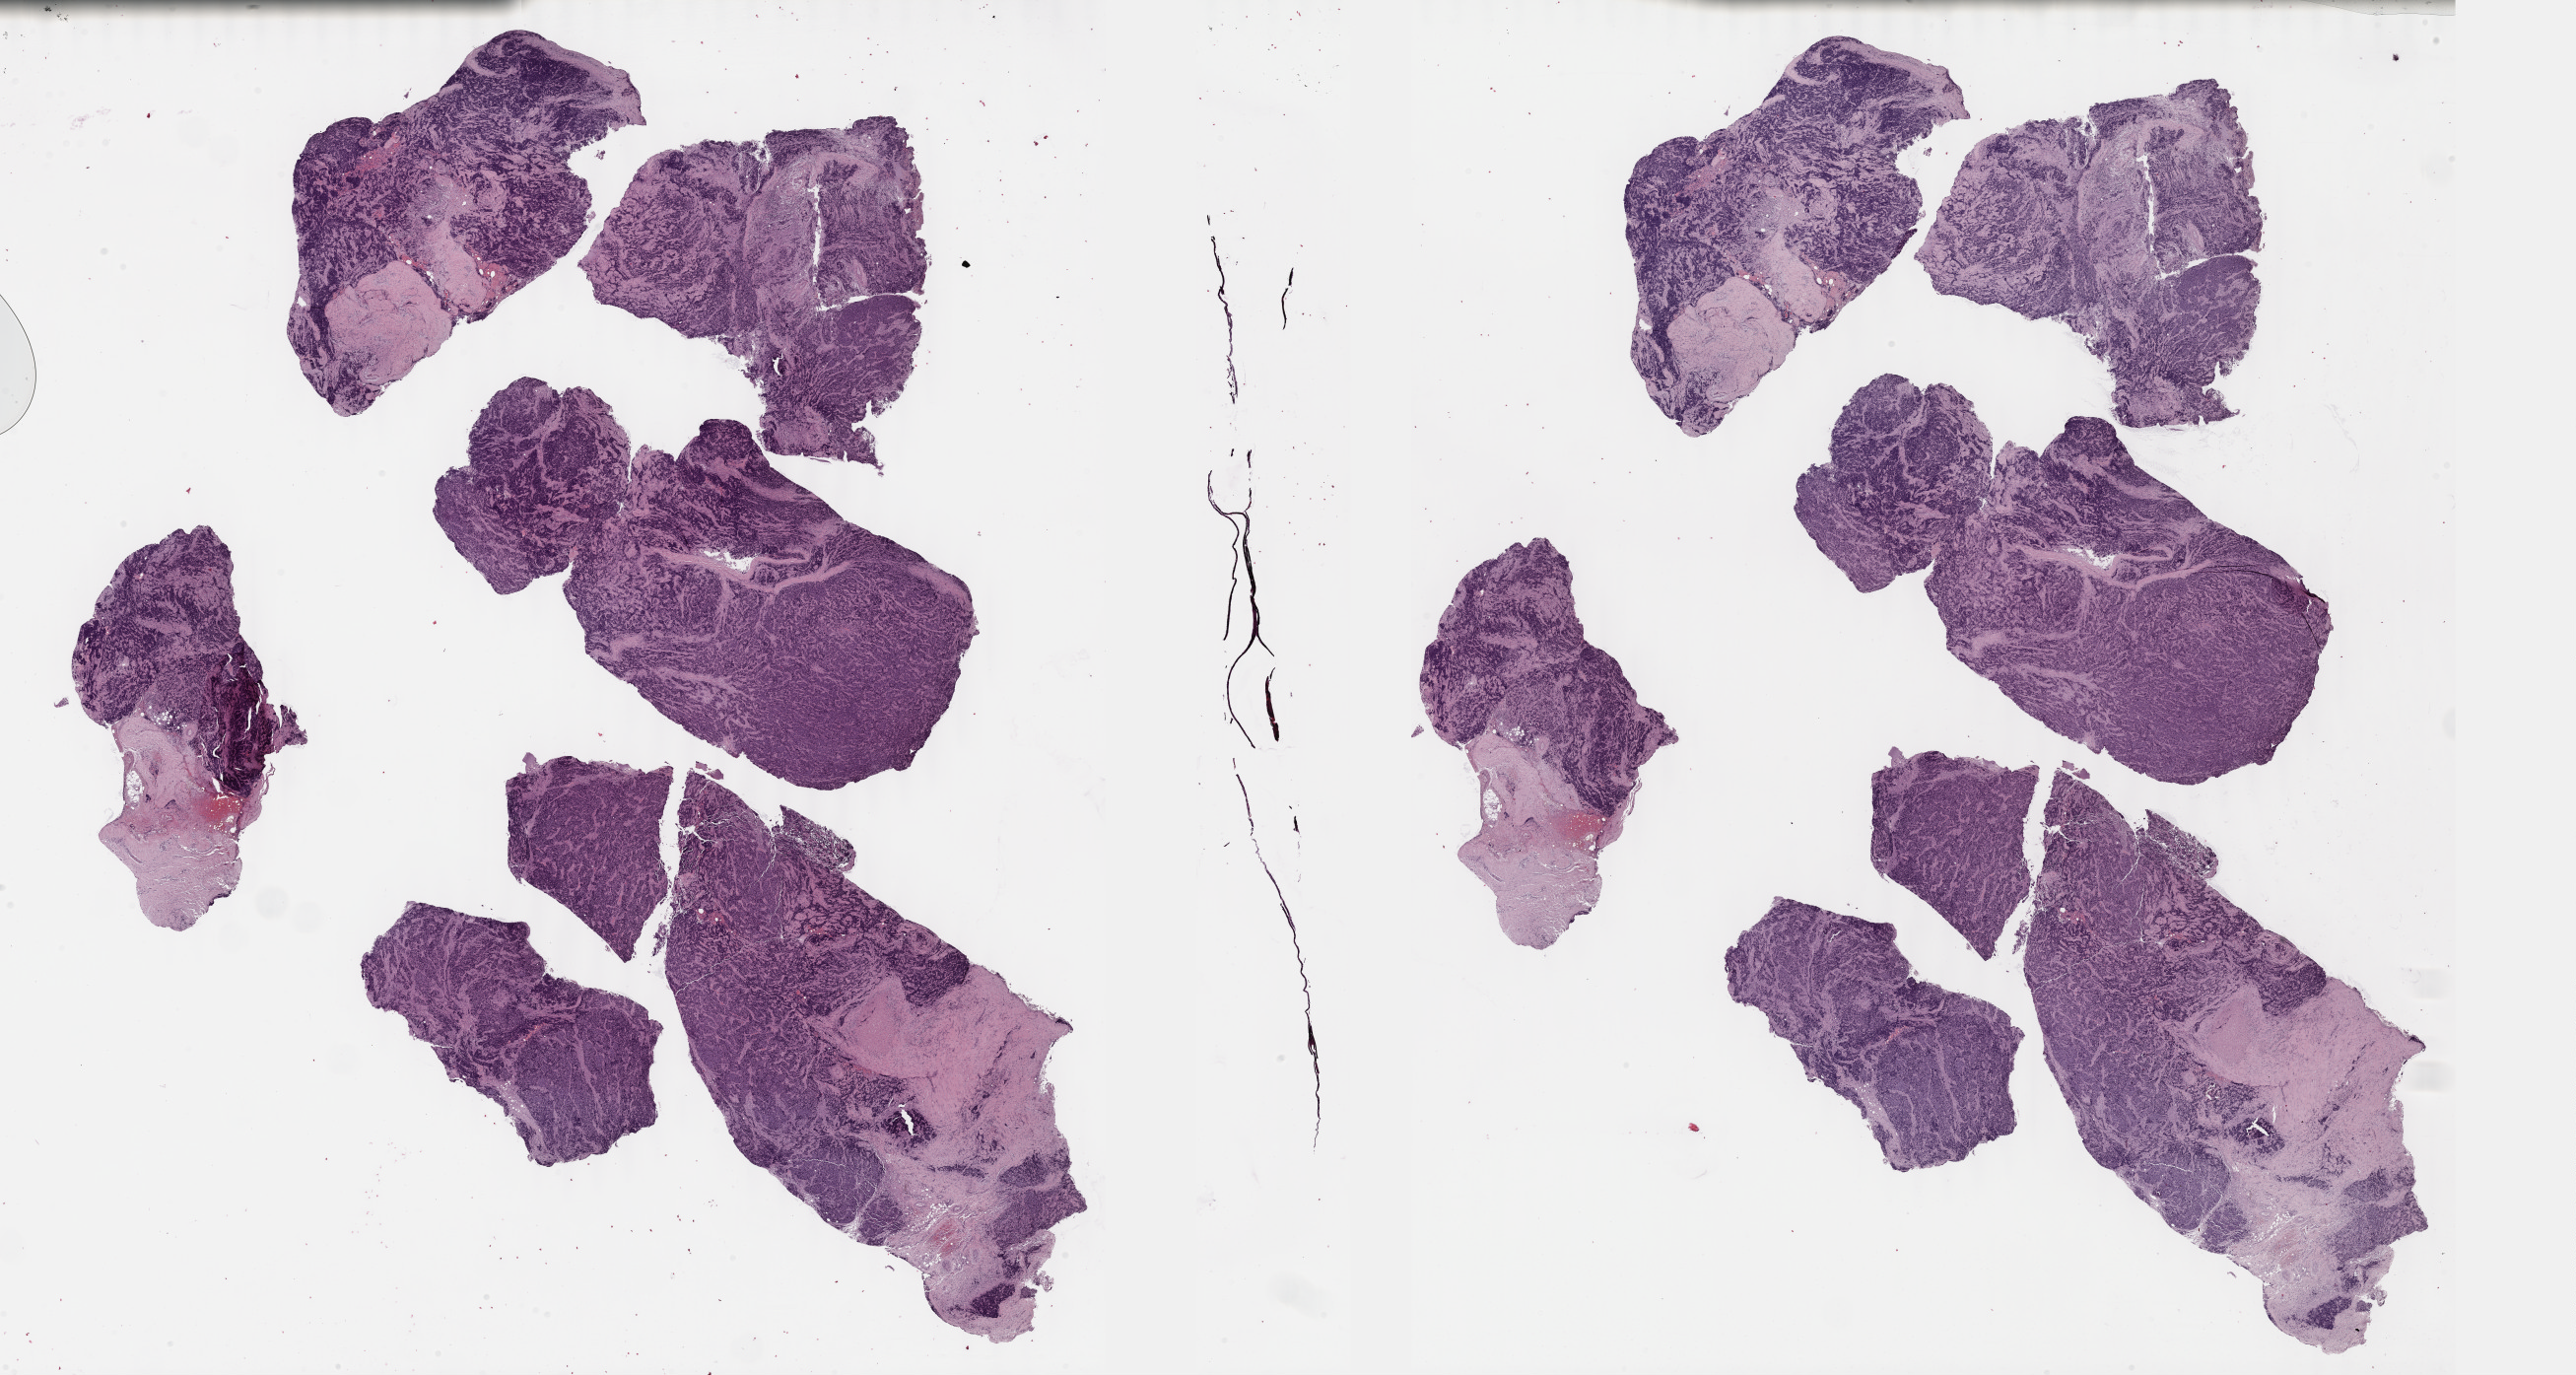
Digitized H&E-stained tissue section (whole slide) — shown as a low-resolution overview of the whole scanned area (about 42.3 x 22.5 mm, acquisition: 40x scan), formalin-fixed paraffin-embedded (FFPE) diagnostic section, sample: primary tumour, thymus. Patient: female, age at initial diagnosis 71 years.
• histologic diagnosis: Thymic carcinoma, NOS (anterior mediastinum)